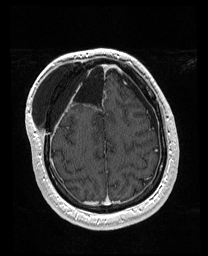
Brain MRI from a brain-tumour surgery series, one axial slice. Slice 51 of 176 in the series (ordered by position). T1-weighted post-contrast. 1 mm slice thickness. 208 × 256 image matrix, field of view 208 × 256 mm. From the clinical record (not read from this slice): histopathology: Astrocytoma; WHO grade: 4; IDH mutation: yes; tumour location: Right Orbitofrontal Anterior Temporal Insular.
Structures marked on this image (expert manual segmentation):
- previous resection cavity: bounding box <56,62,106,104> (left, top, right, bottom; pixels)